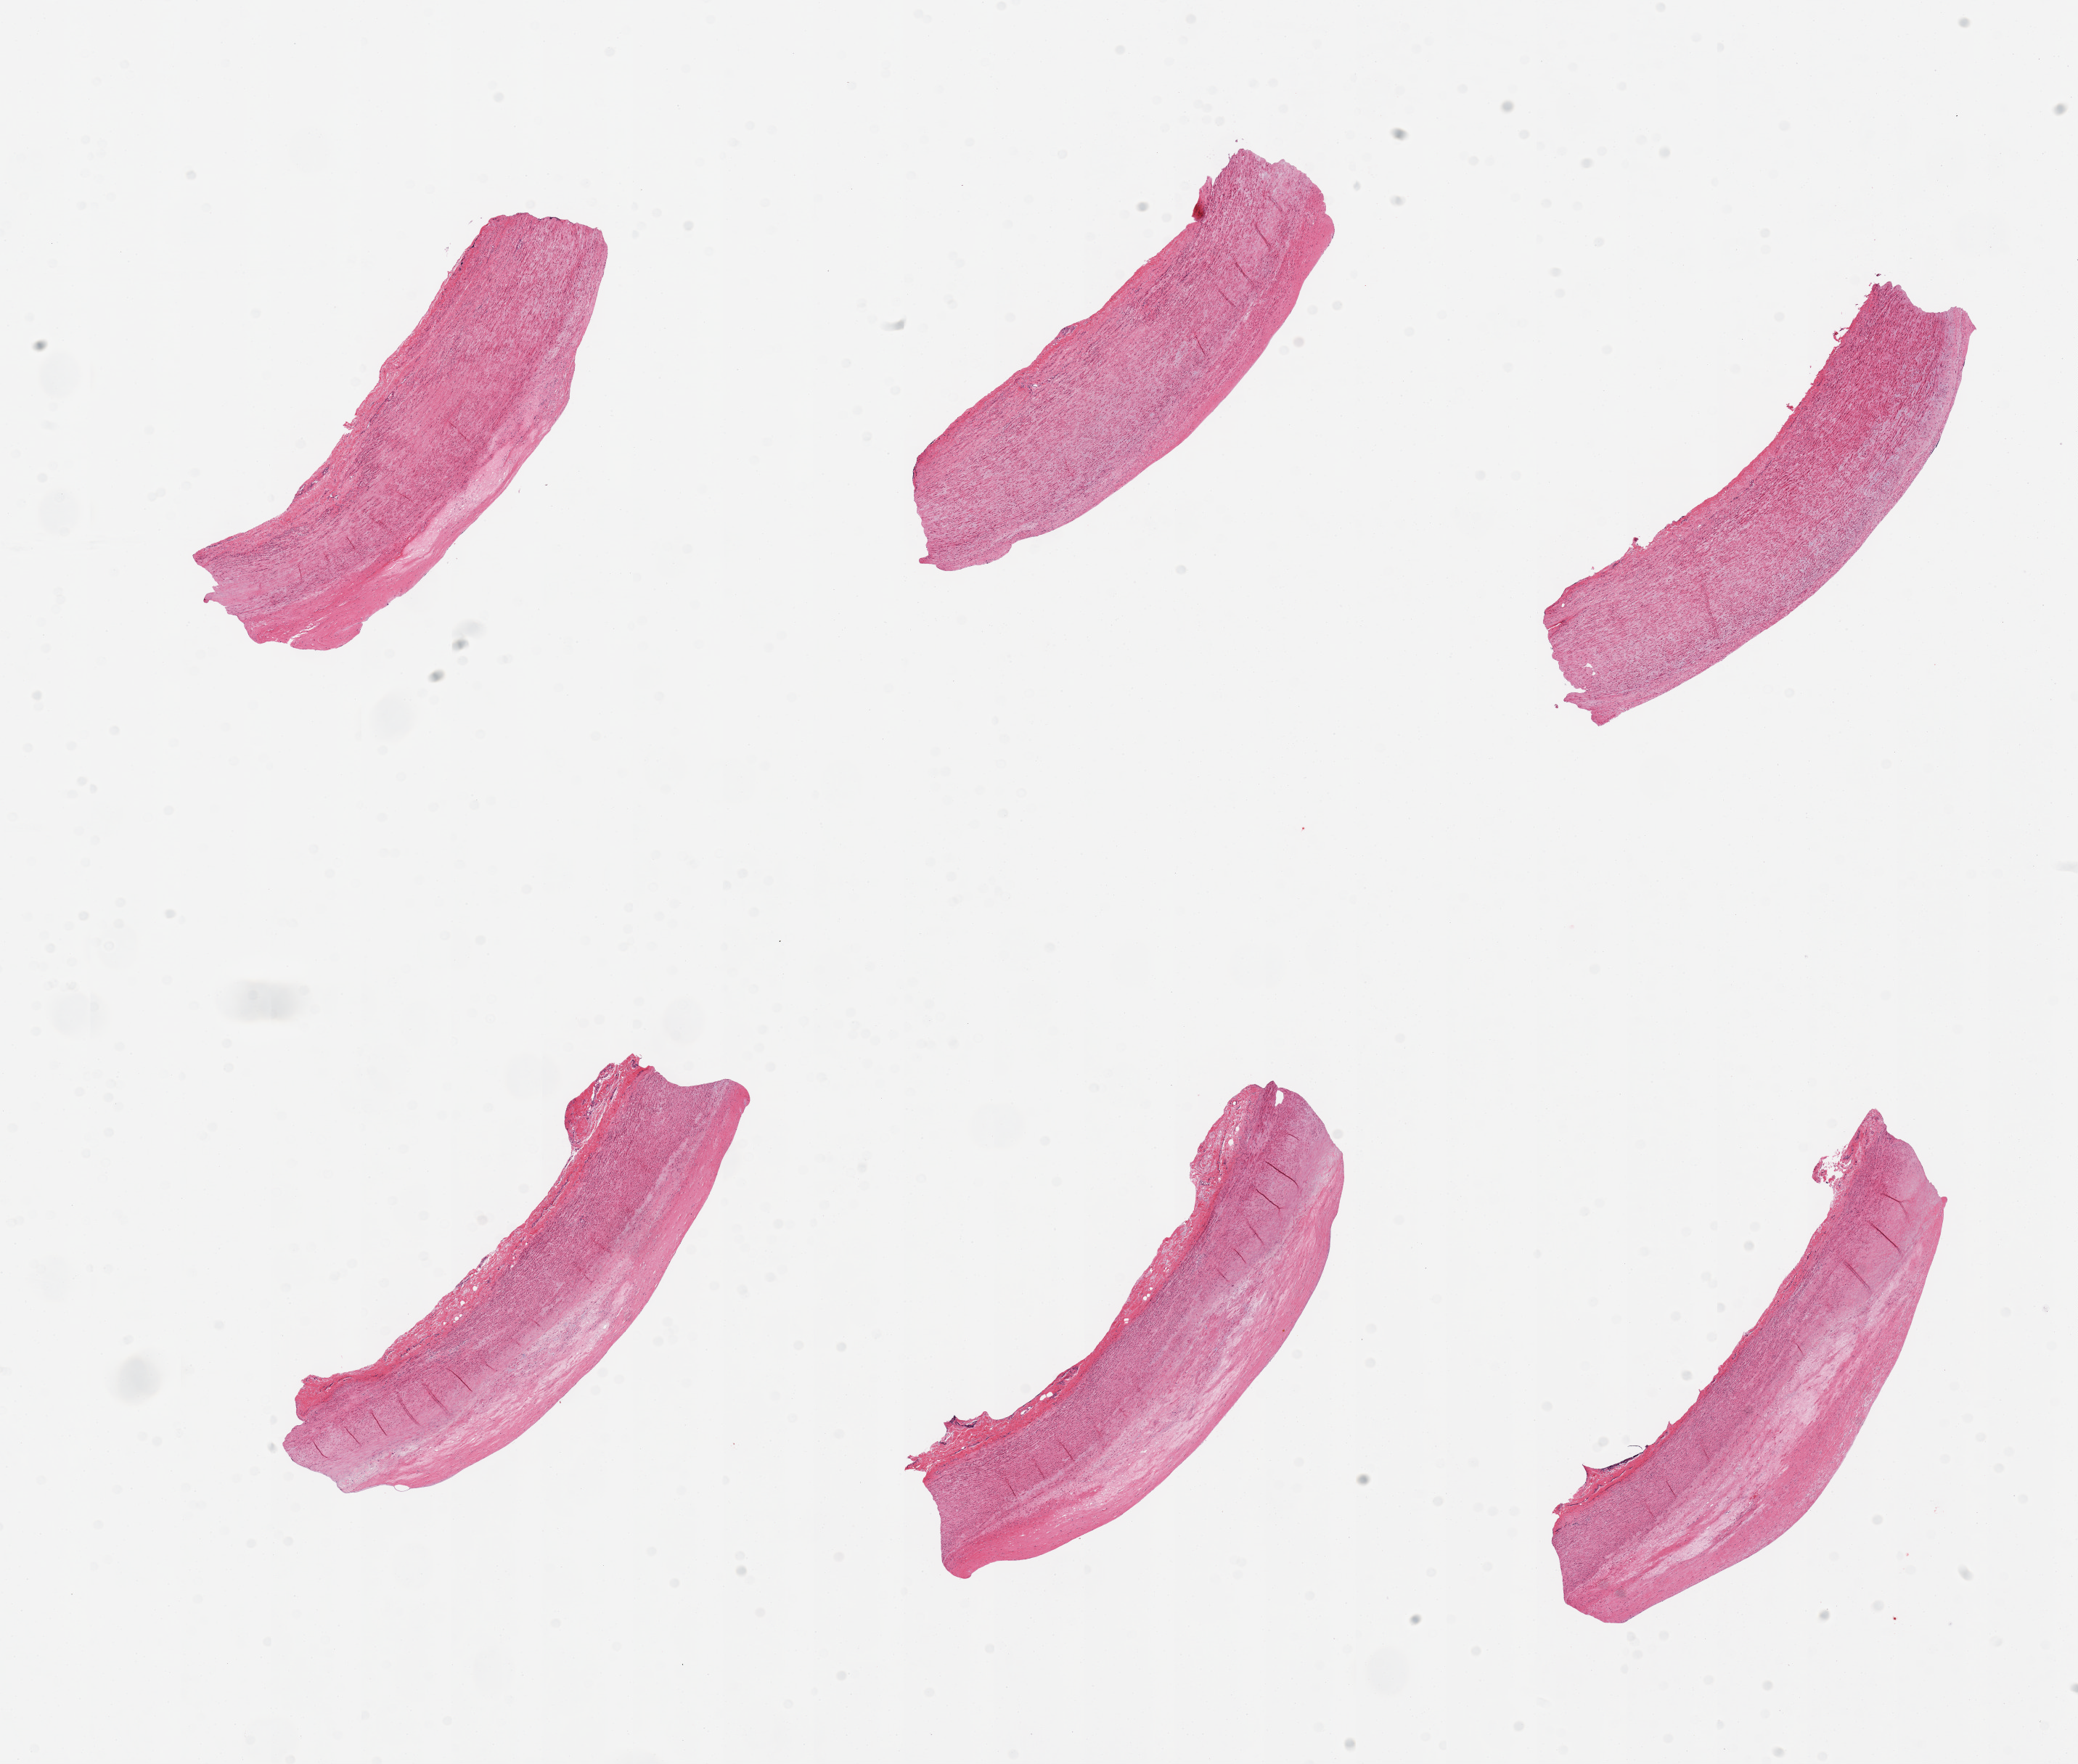
Whole-slide image, haematoxylin and eosin stain, a low-resolution overview of the entire scanned area, about 22.6 x 19.2 mm (acquisition: 20x scan). PAXgene-fixed paraffin-embedded (PFPE) section. Section of aorta (target tissue). Tissue donor sample. Donor sex: female.
• pathologist's review note for this sample: 6 pieces; flat fibrofatty plaques